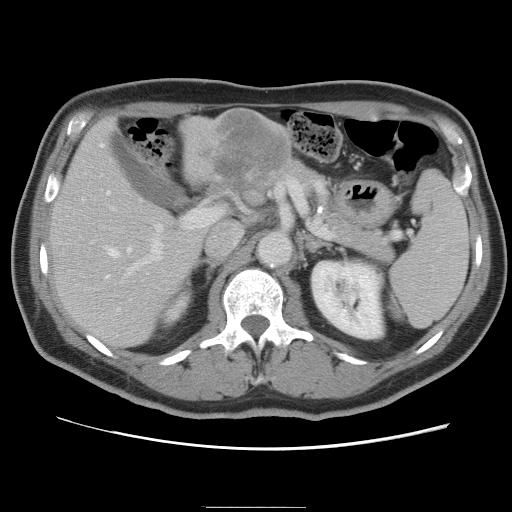
Contrast-enhanced abdominal CT, one axial slice; slice 47 of 87 in the series (ordered by position); 120 kVp; soft-tissue window (W 400 / L 40 HU); 512 × 512 image matrix. Male patient, age 63 years. Case-level facts recorded for this patient, not image findings: diagnosis: colorectal cancer liver metastases, imaged before liver resection; multiple liver metastases: no; largest metastasis: 9 cm; disease in both lobes: no.
Annotated regions visible in this slice (expert manual segmentation):
- hepatic veins: bounding box (x1, y1, x2, y2) in pixels: (101, 144, 131, 278)
- liver: (51, 108, 293, 348)
- planned liver remnant (the part of the liver to remain after resection): (50, 146, 201, 347)
- portal vein (with intrahepatic branches): (110, 206, 205, 283)
- liver metastasis: (214, 114, 283, 189)